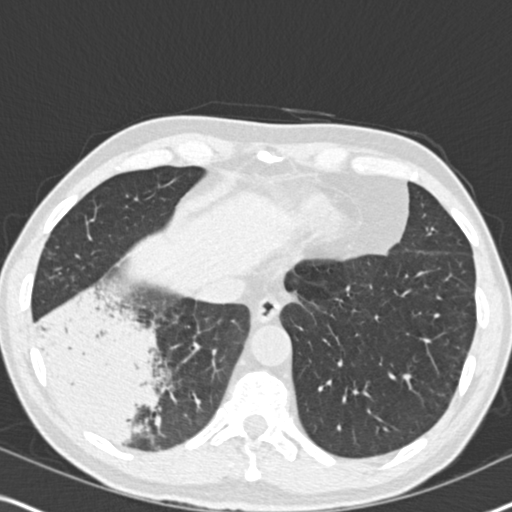
Low-dose screening chest CT, one axial slice; slice 59 of 182 in the series (ordered by position); 120 kVp; lung window (W 1500 / L -600 HU); 512 × 512 image matrix, field of view 330 × 330 mm.
Outlined on this slice (manually delineated by an expert):
- lesion 1 (tumor, lower lobe of right lung): bounding box (x1, y1, x2, y2) in pixels: (40, 292, 153, 436)